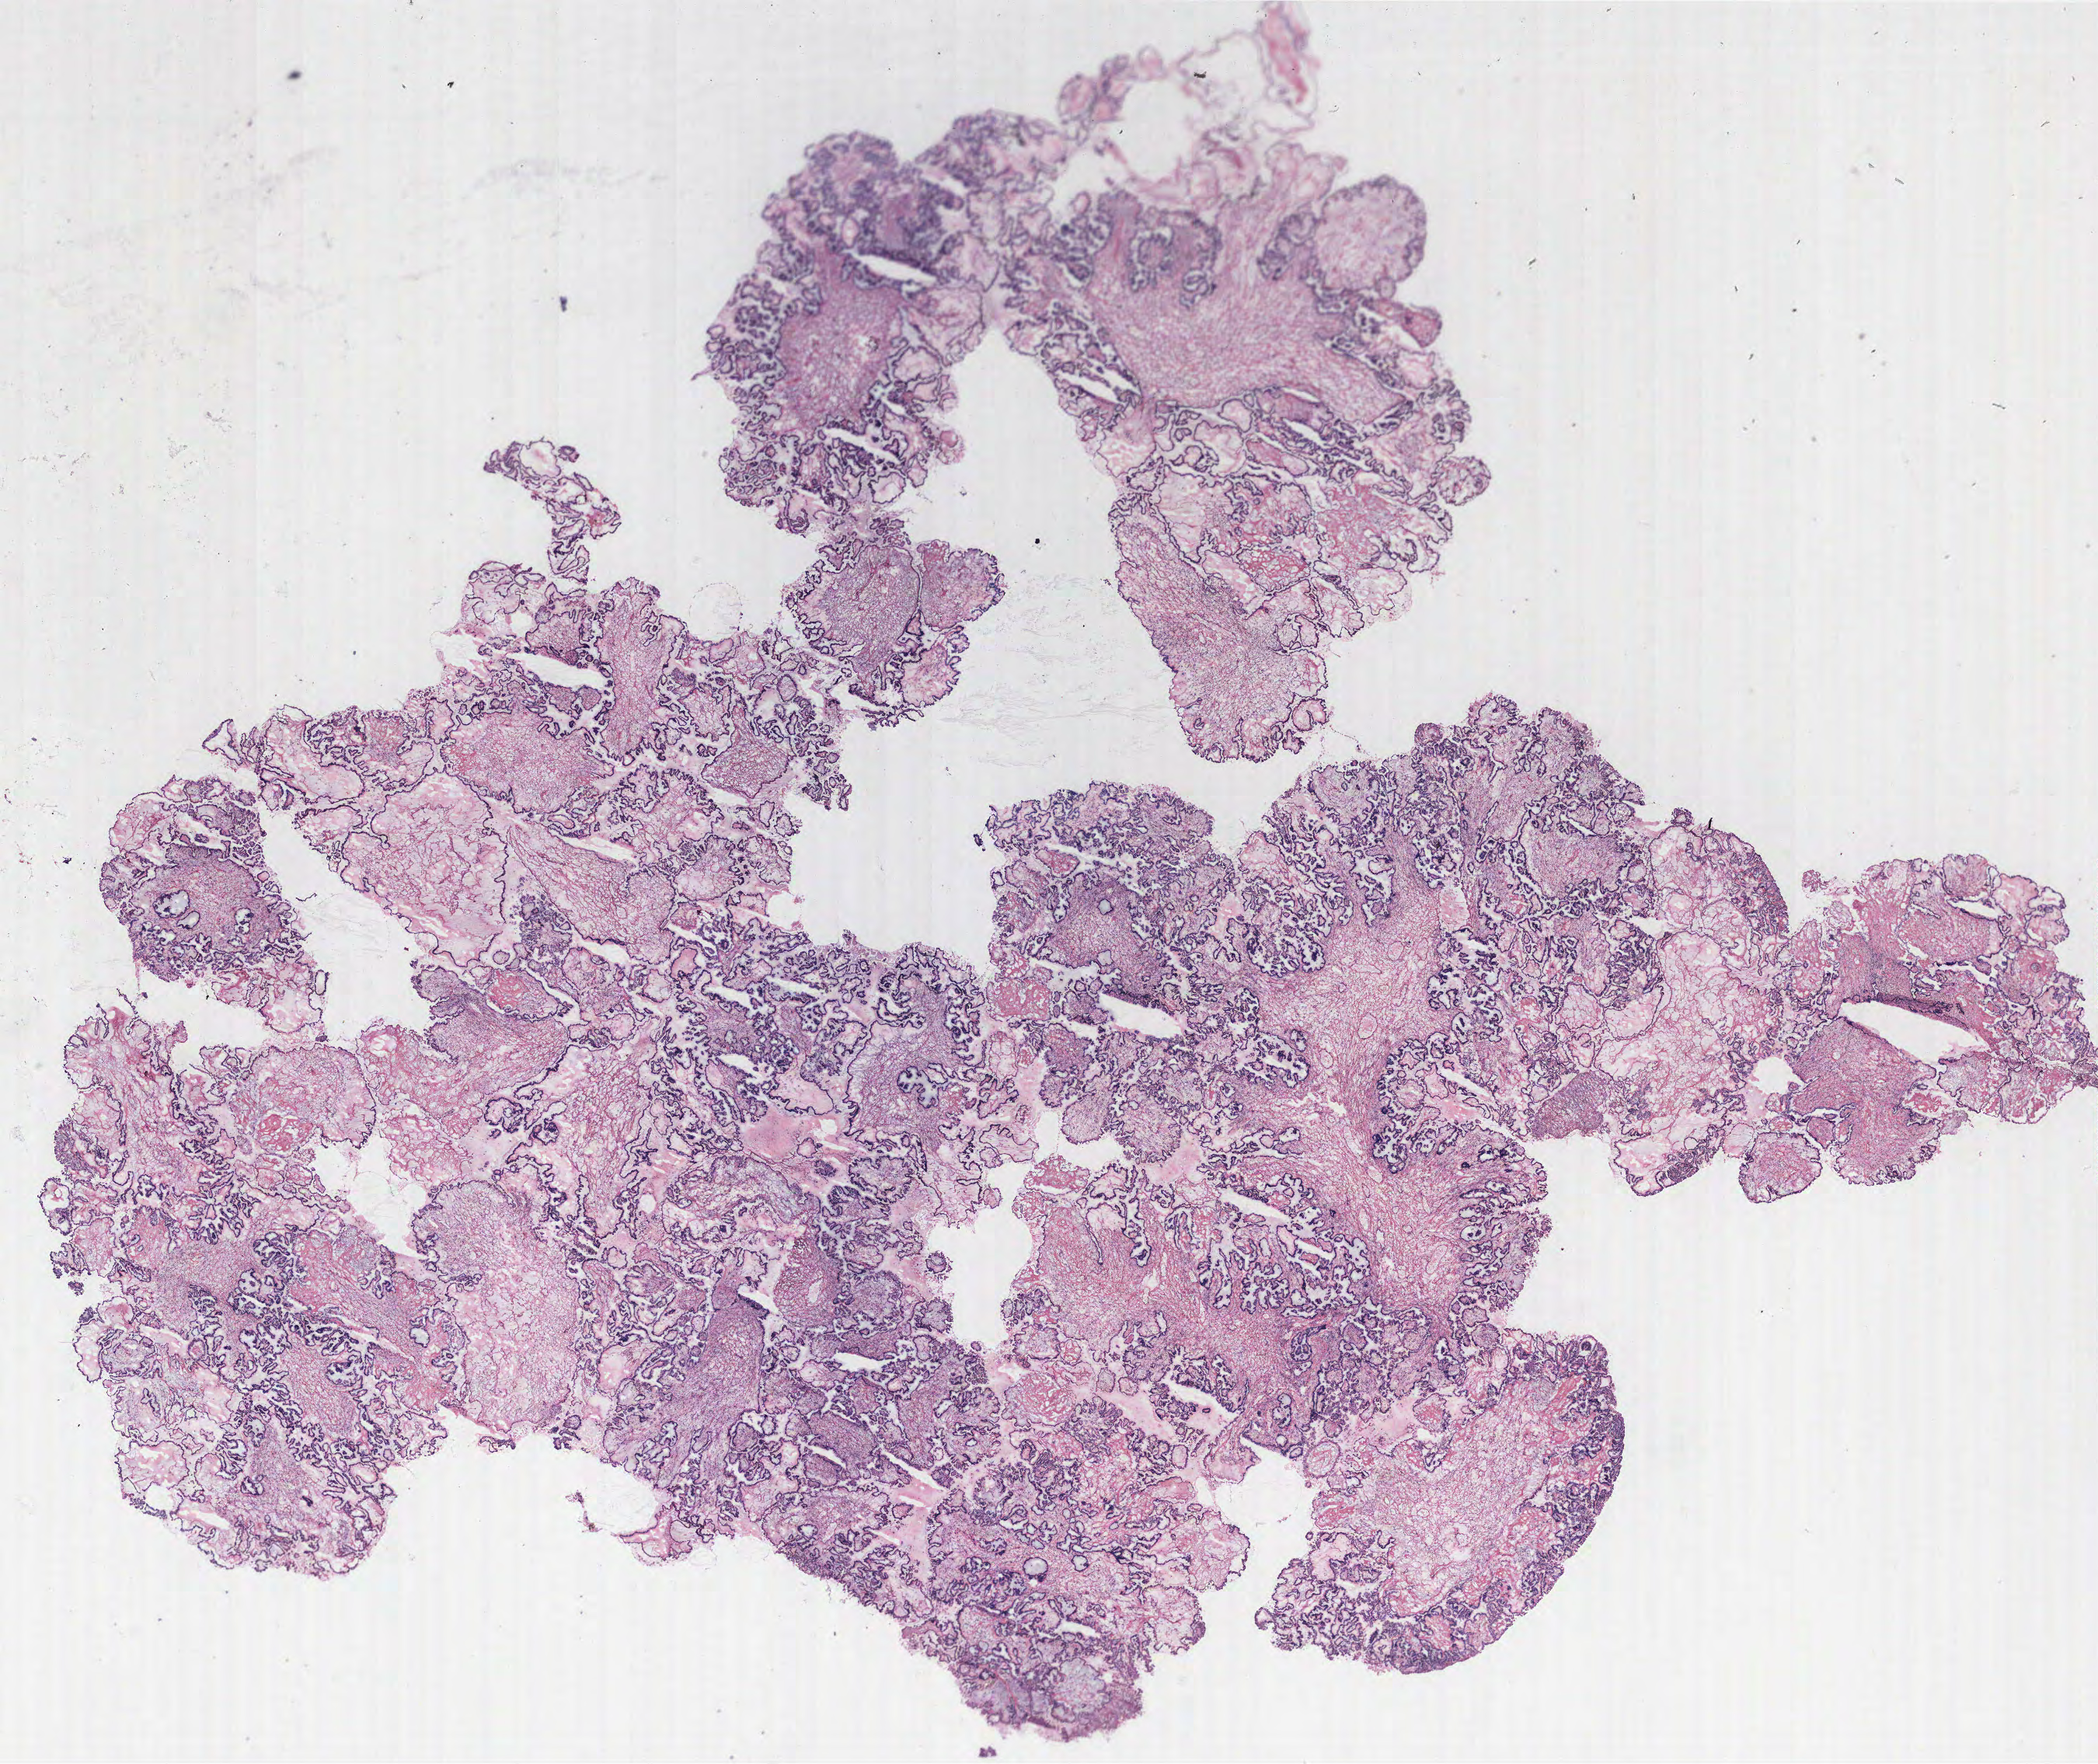
Digitized H&E tissue section (whole slide), whole scanned area (about 21.6 x 18.2 mm) shown as a low-resolution overview; tumour tissue sample, ovary. Patient: female, age 49 years.
Primary tumour site (as recorded): ovary. Histologic diagnosis: Serous adenocarcinoma, NOS.